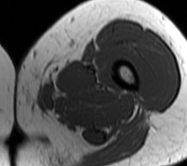
MRI of an extremity soft-tissue mass, one axial slice; slice 5 of 62 in the series (ordered by position); MR volume resampled by the dataset authors to the PET/CT grid (not the native acquisition matrix); 3.27 mm slice thickness; 187 × 166 image matrix, field of view 183 × 162 mm. Female patient. Case-level facts recorded for this patient, not image findings: histological type: leiomyosarcoma; grade: high; site of the primary tumour: groin.
Outlined on this slice (expert contour drawn on MRI and transferred to this co-registered scan by the dataset authors):
- gross tumour volume including surrounding oedema: bounding box [x1, y1, x2, y2] px = [16, 91, 44, 113]